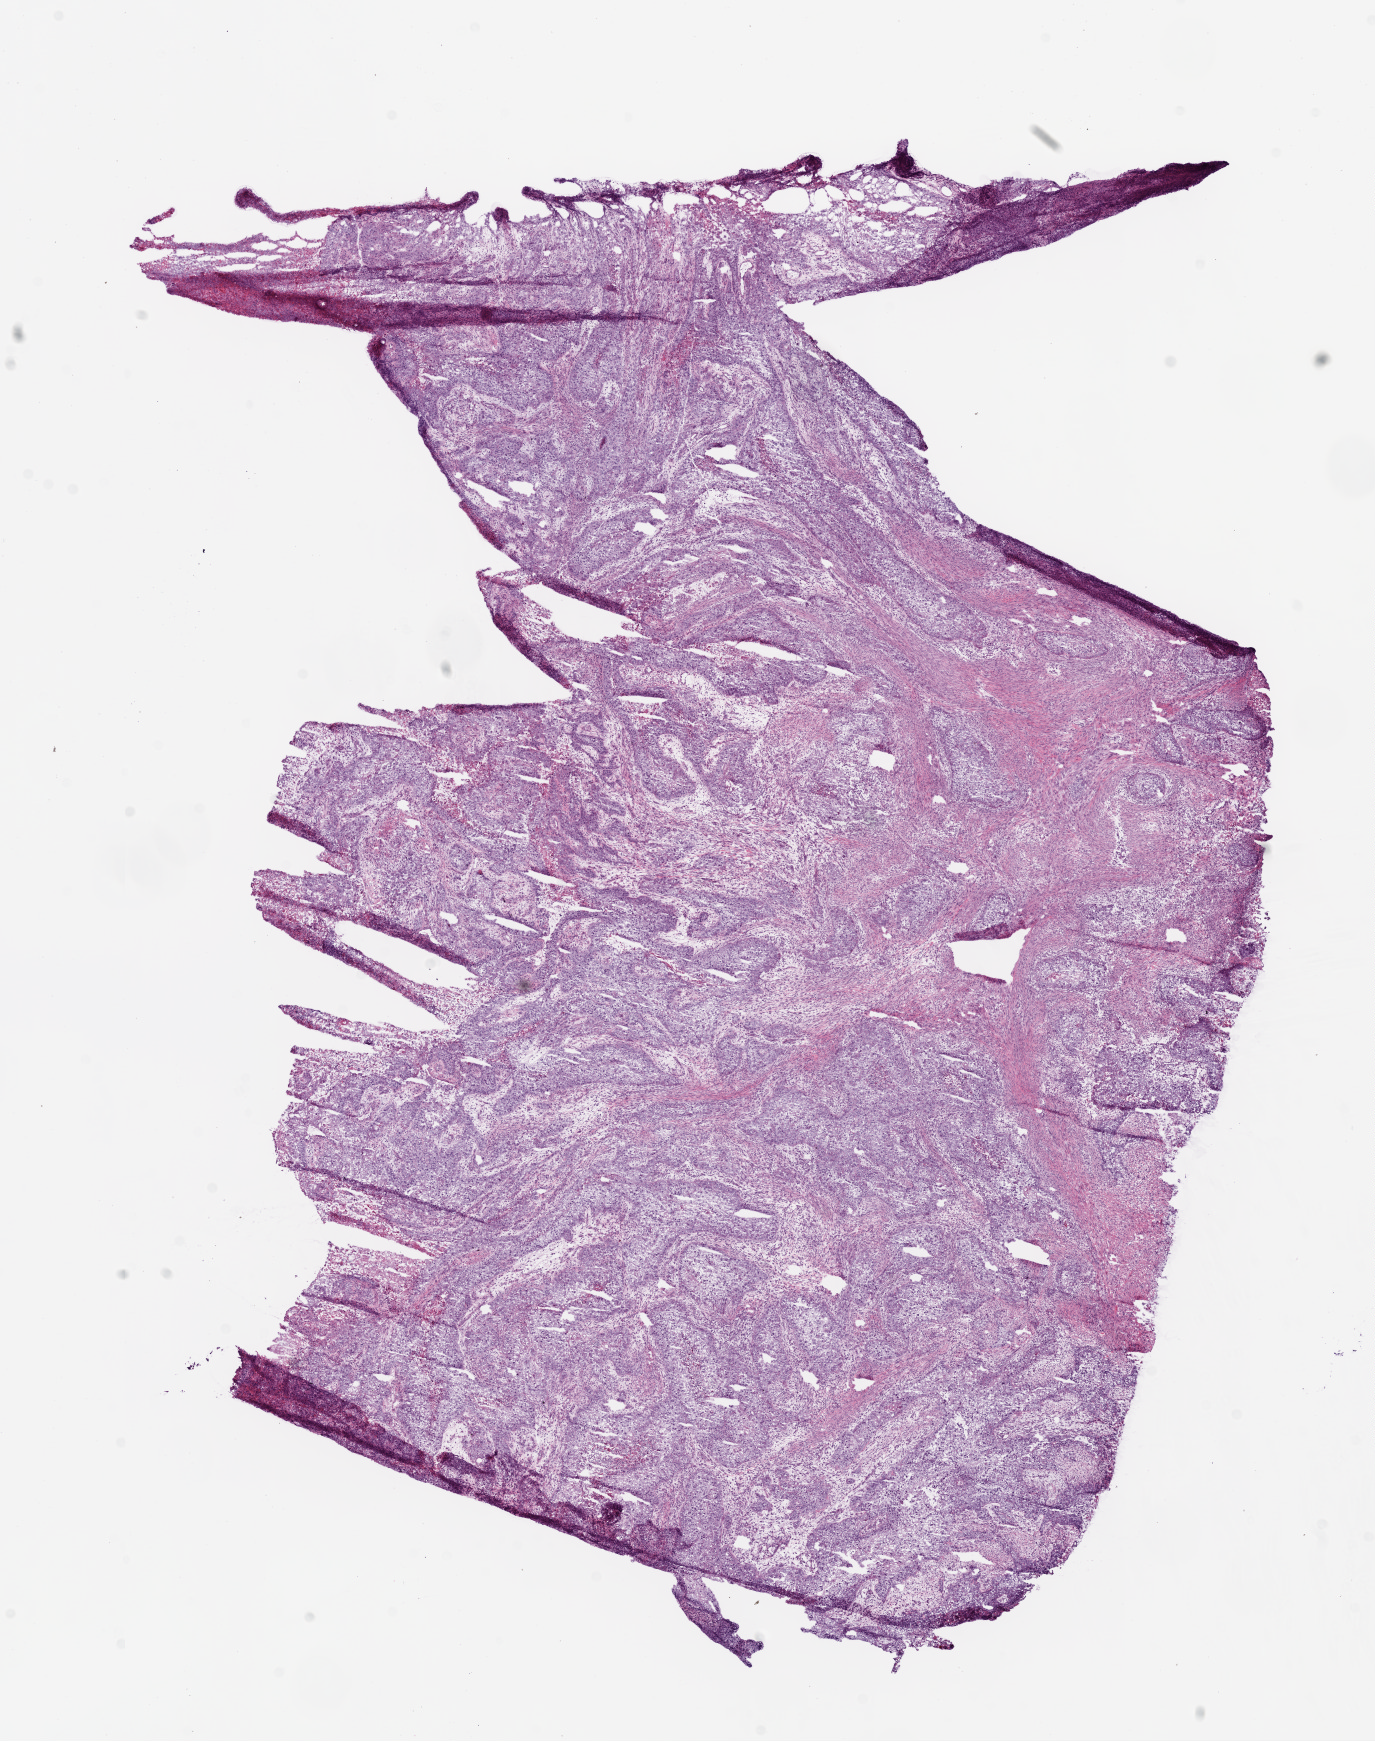
Hematoxylin and eosin (H&E) stained whole-slide image — low-resolution overview of the scanned area, about 11.0 x 14.0 mm, frozen section from the bottom of the tissue portion, primary tumour sample from the lung. Male patient; age at initial diagnosis 47 years.
Pathologic diagnosis: Squamous cell carcinoma, NOS.